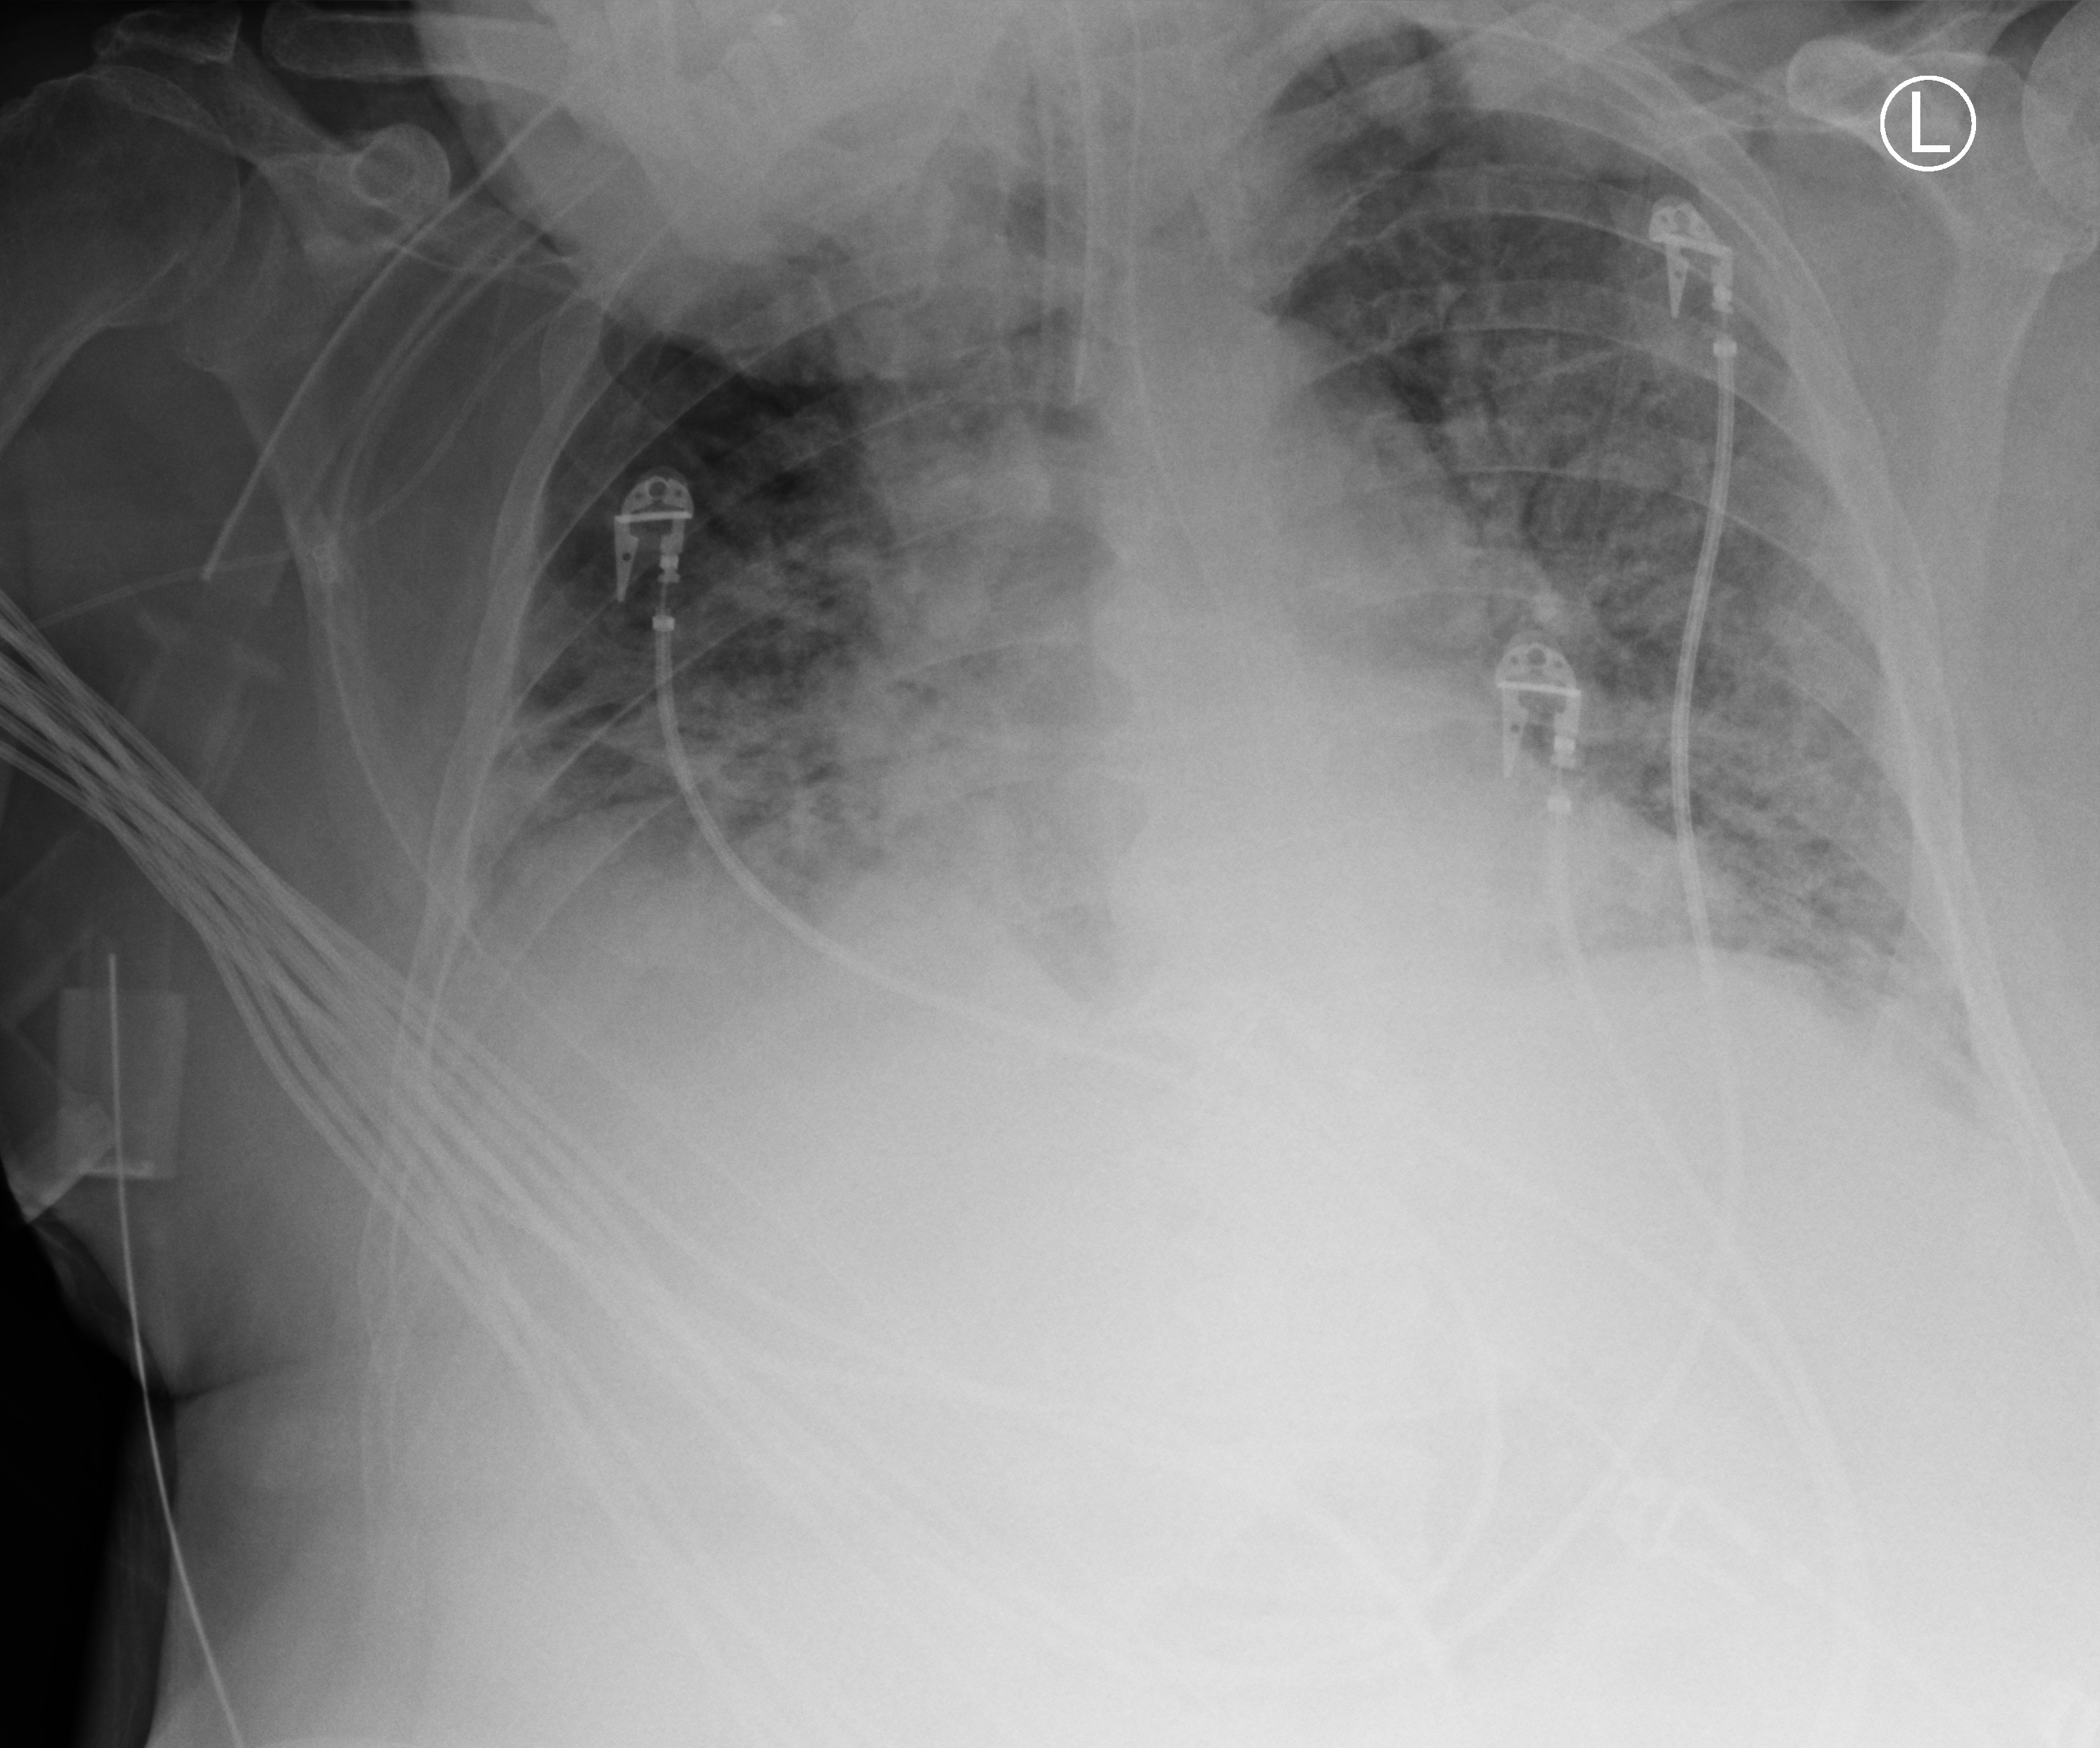
Bedside chest radiograph (computed radiography); anteroposterior (AP) projection. Male patient hospitalised with COVID-19, age 60–74 years.
From the hospital-stay record, not from the radiograph (when in the stay this image was taken is not recorded): admitted to intensive care during this hospital stay: yes; mechanically ventilated during this hospital stay: yes.